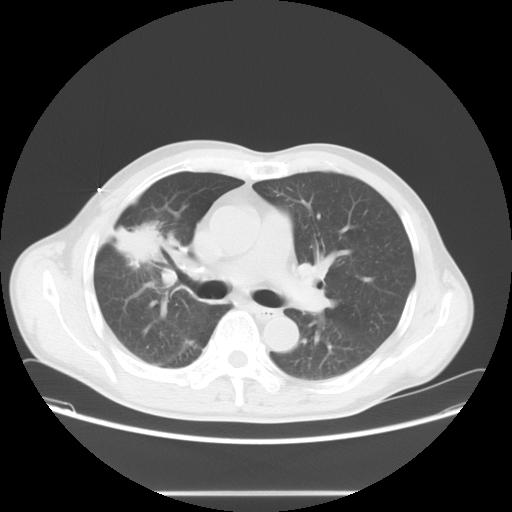
Chest CT, one axial slice; slice 43 of 71 in the series (ordered by position); reconstruction kernel STANDARD; 120 kVp; lung window (W 1500 / L -600 HU); 5 mm slice thickness; 512 × 512 image matrix, field of view 392 × 392 mm. Patient: male, 67 years. From the clinical record (not read from this slice): clinical TNM (as recorded): T2 N0 M0.
Annotated regions visible in this slice (bounding box drawn by a radiologist):
- lung tumour (recorded histology: adenocarcinoma): bounding box <112,225,158,266> (left, top, right, bottom; pixels)